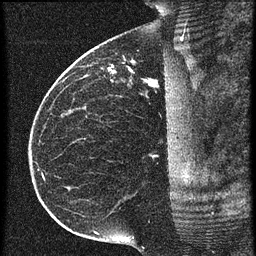
Breast MRI (dynamic contrast-enhanced), one sagittal slice; slice 36 of 60 in the series (ordered by position); 3 images stored at this slice position (order not interpretable as contrast timing); 1.5 T; TE 4.2 ms, TR 20.4 ms; 1.5 mm slice thickness; 256 × 256 image matrix, field of view 200 × 200 mm. Patient: female, 35 years. Case-level facts recorded for this patient, not image findings: setting: breast cancer imaged before/during neoadjuvant chemotherapy; receptor status: HR-positive, HER2-negative.
Outlined on this slice (semi-automatically segmented with operator editing):
- analysis volume of interest (the breast-tissue region the enhancement analysis was run in; not a lesion): bounding box [x1, y1, x2, y2] px = [84, 50, 179, 97]
- tumour enhancement mask (voxels above the 90 % enhancement threshold inside the analysis volume of interest): [146, 80, 153, 85]